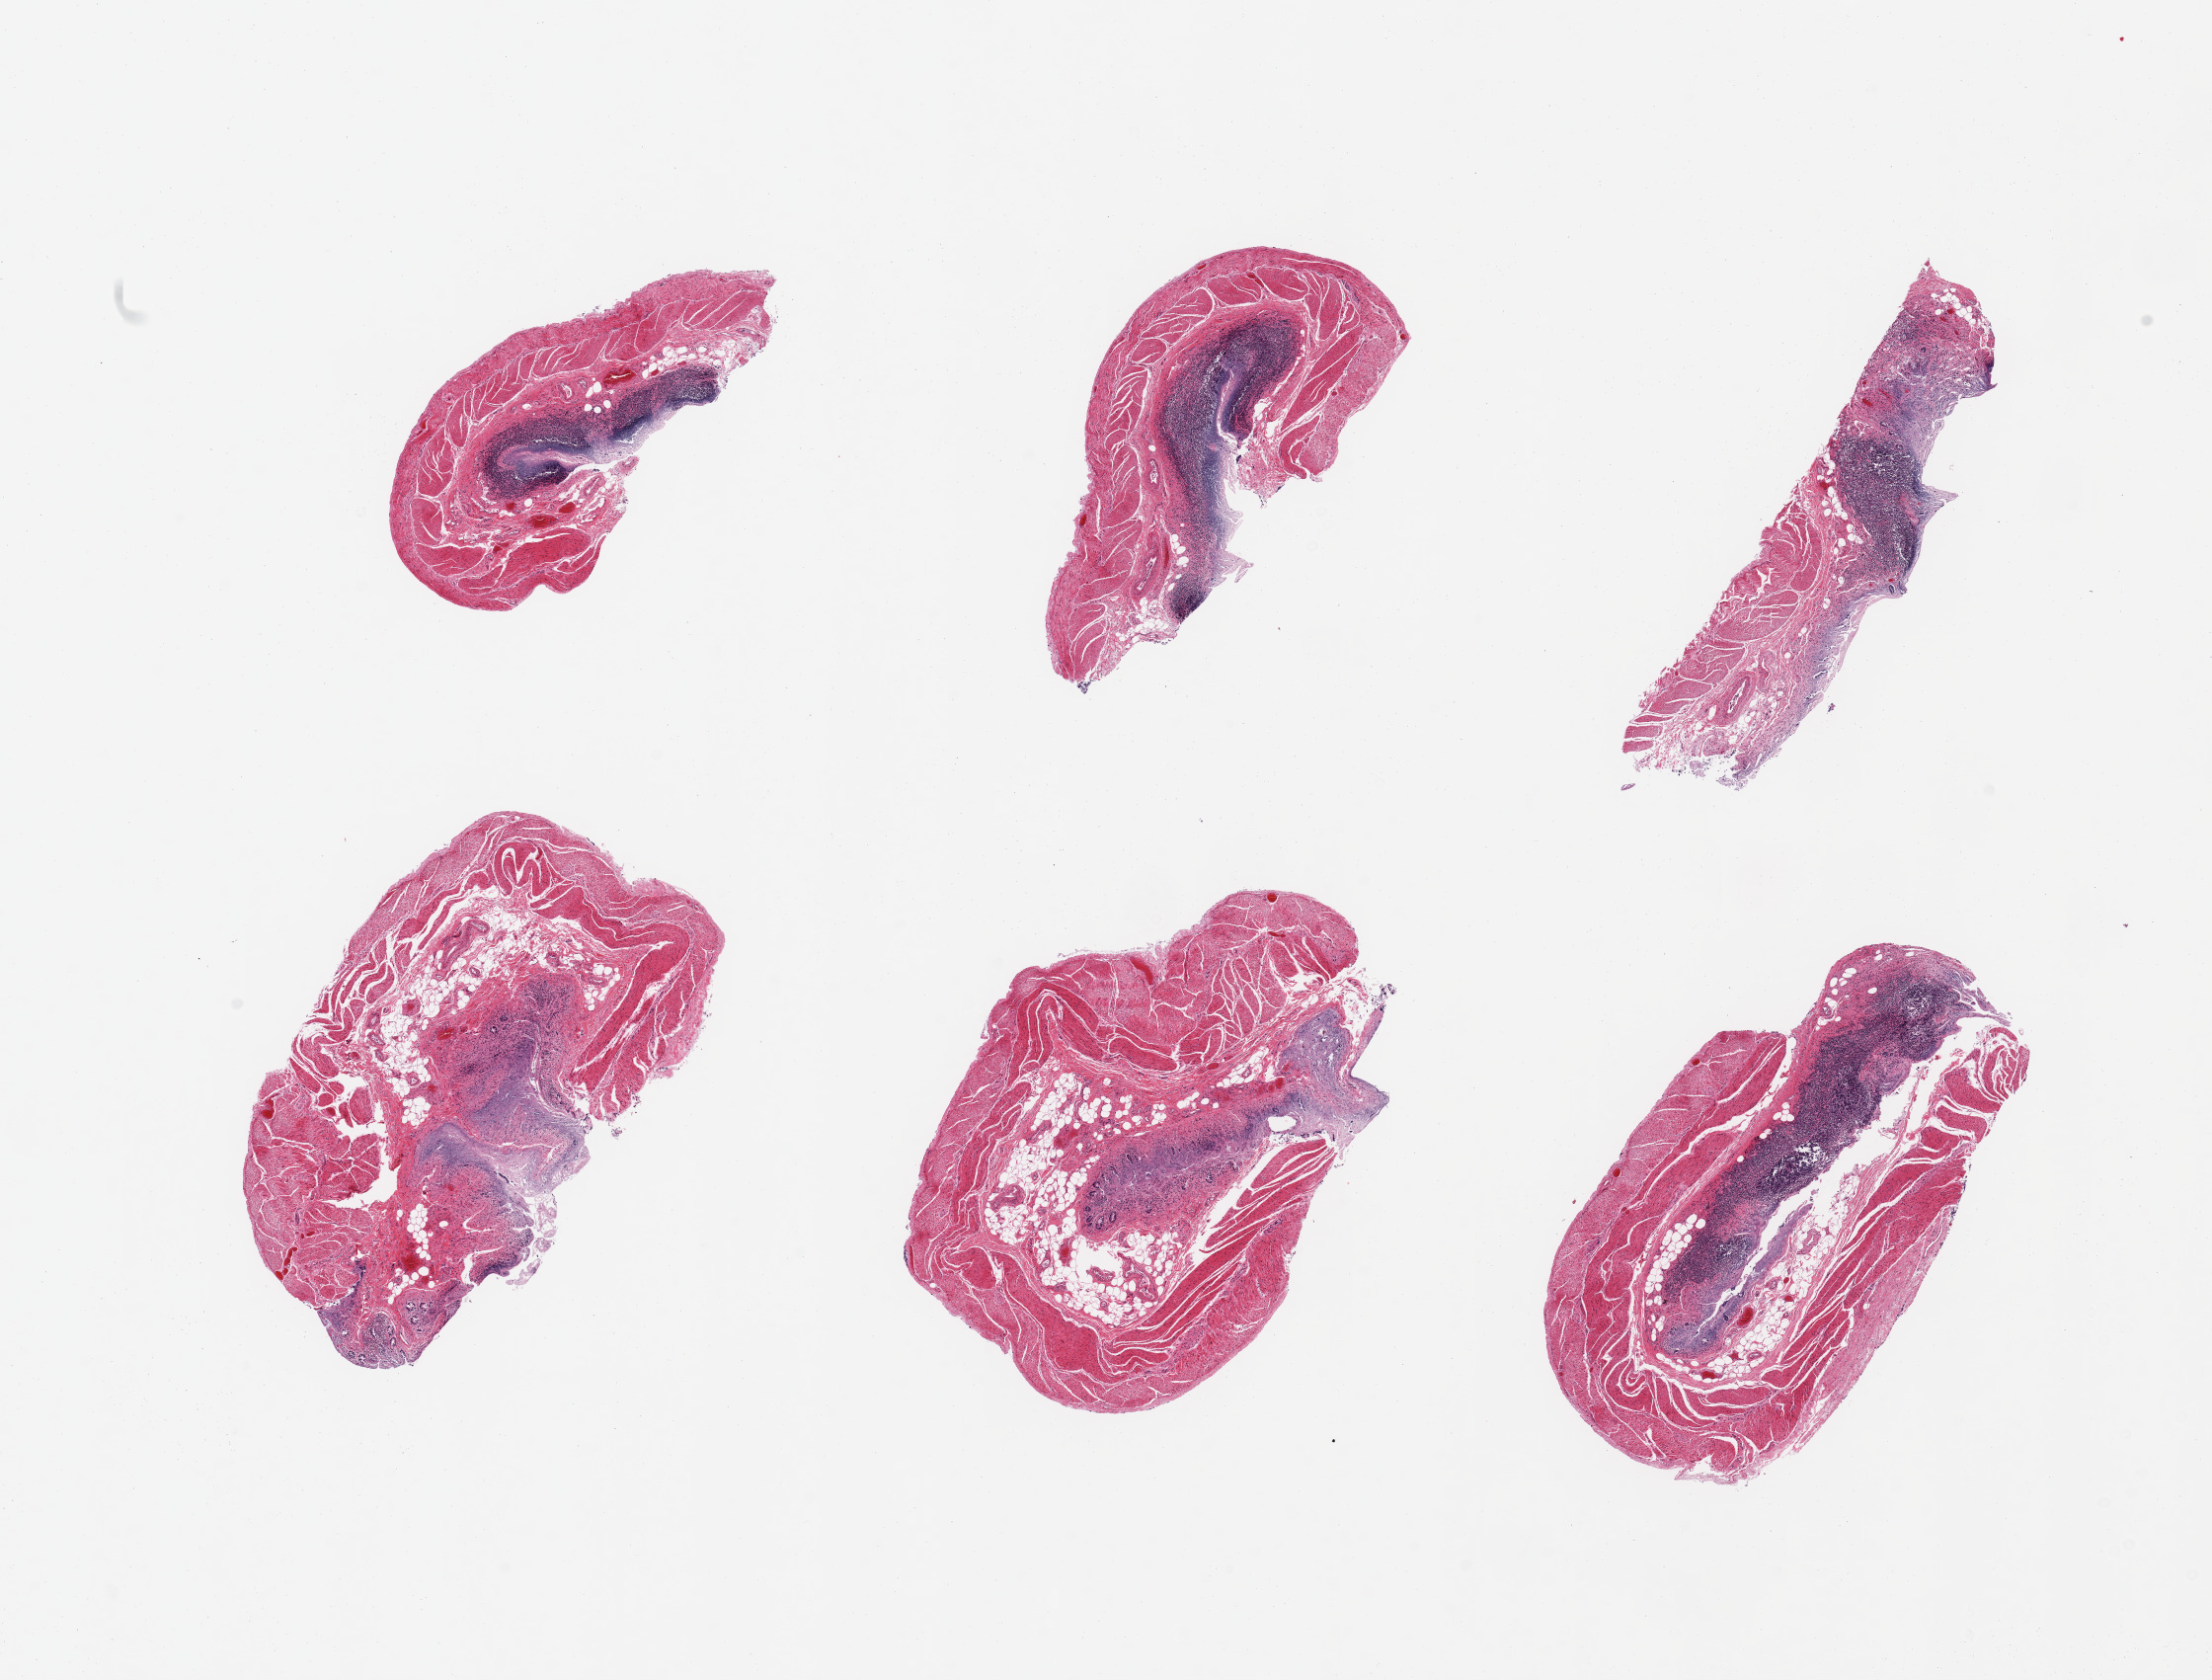
Whole-slide image, haematoxylin and eosin stain, brightfield — a low-resolution overview of the entire scanned area, about 17.7 x 13.5 mm; PAXgene-fixed paraffin-embedded (PFPE) section; sampled site (target tissue): ileum; tissue donor sample. Donor: male.
* reviewer comment on this tissue sample: 6 pieces, target lymphoid aggregates up to ~30%